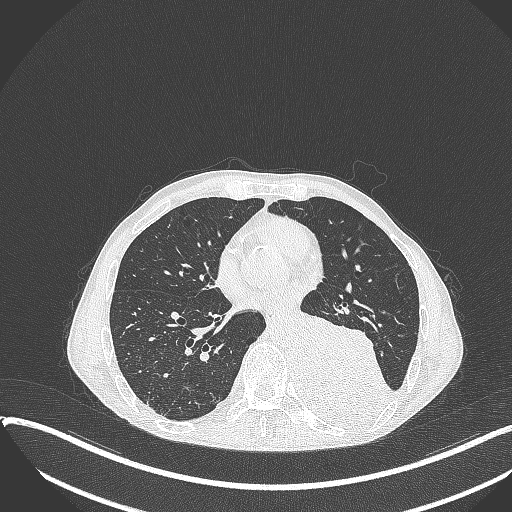
Chest CT, one axial slice; slice 155 of 401 in the series (ordered by position); reconstruction kernel B70f; lung window (W 1500 / L -600 HU); 512 × 512 image matrix. Male patient, age 57 years. From the clinical record (not read from this slice): clinical TNM (as recorded): T4 N0 M0.
Structures marked on this image (bounding box drawn by a radiologist):
- lung tumour (recorded histology: squamous cell carcinoma): bounding box <293,307,397,424> (left, top, right, bottom; pixels)